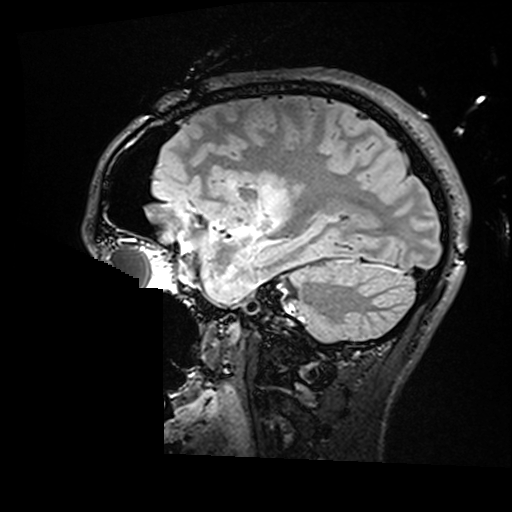
Brain MRI from a brain-tumour surgery series, one sagittal slice. Position 112 of 176 along the scan axis. T2 FLAIR. 512 × 512 image matrix, field of view 250 × 250 mm. Case-level facts recorded for this patient, not image findings: histopathology: Astrocytoma; WHO grade: 2; IDH mutation: yes.
Structures marked on this image (manually delineated by an expert):
- residual tumour: bounding box <260,183,287,224> (left, top, right, bottom; pixels)